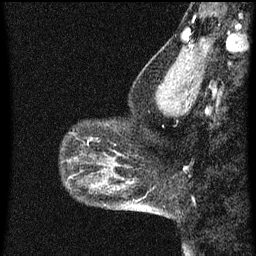
Breast MRI (dynamic contrast-enhanced), one sagittal slice. Position 16 of 60 along the scan axis. Dynamic contrast-enhanced series, image 2 of 3 at this slice position (ordered by acquisition). 1.5 T. TE 4.2 ms, TR 8 ms. 2 mm slice thickness. 256 × 256 image matrix. Female patient, age 43 years.
Structures marked on this image (semi-automatic segmentation, software-assisted and operator-edited):
- analysis volume of interest (the breast-tissue region the enhancement analysis was run in; not a lesion): bounding box (x1, y1, x2, y2) in pixels: (63, 120, 101, 151)
- tumour enhancement mask (voxels above the 70 % enhancement threshold inside the analysis volume of interest): (90, 138, 92, 141)